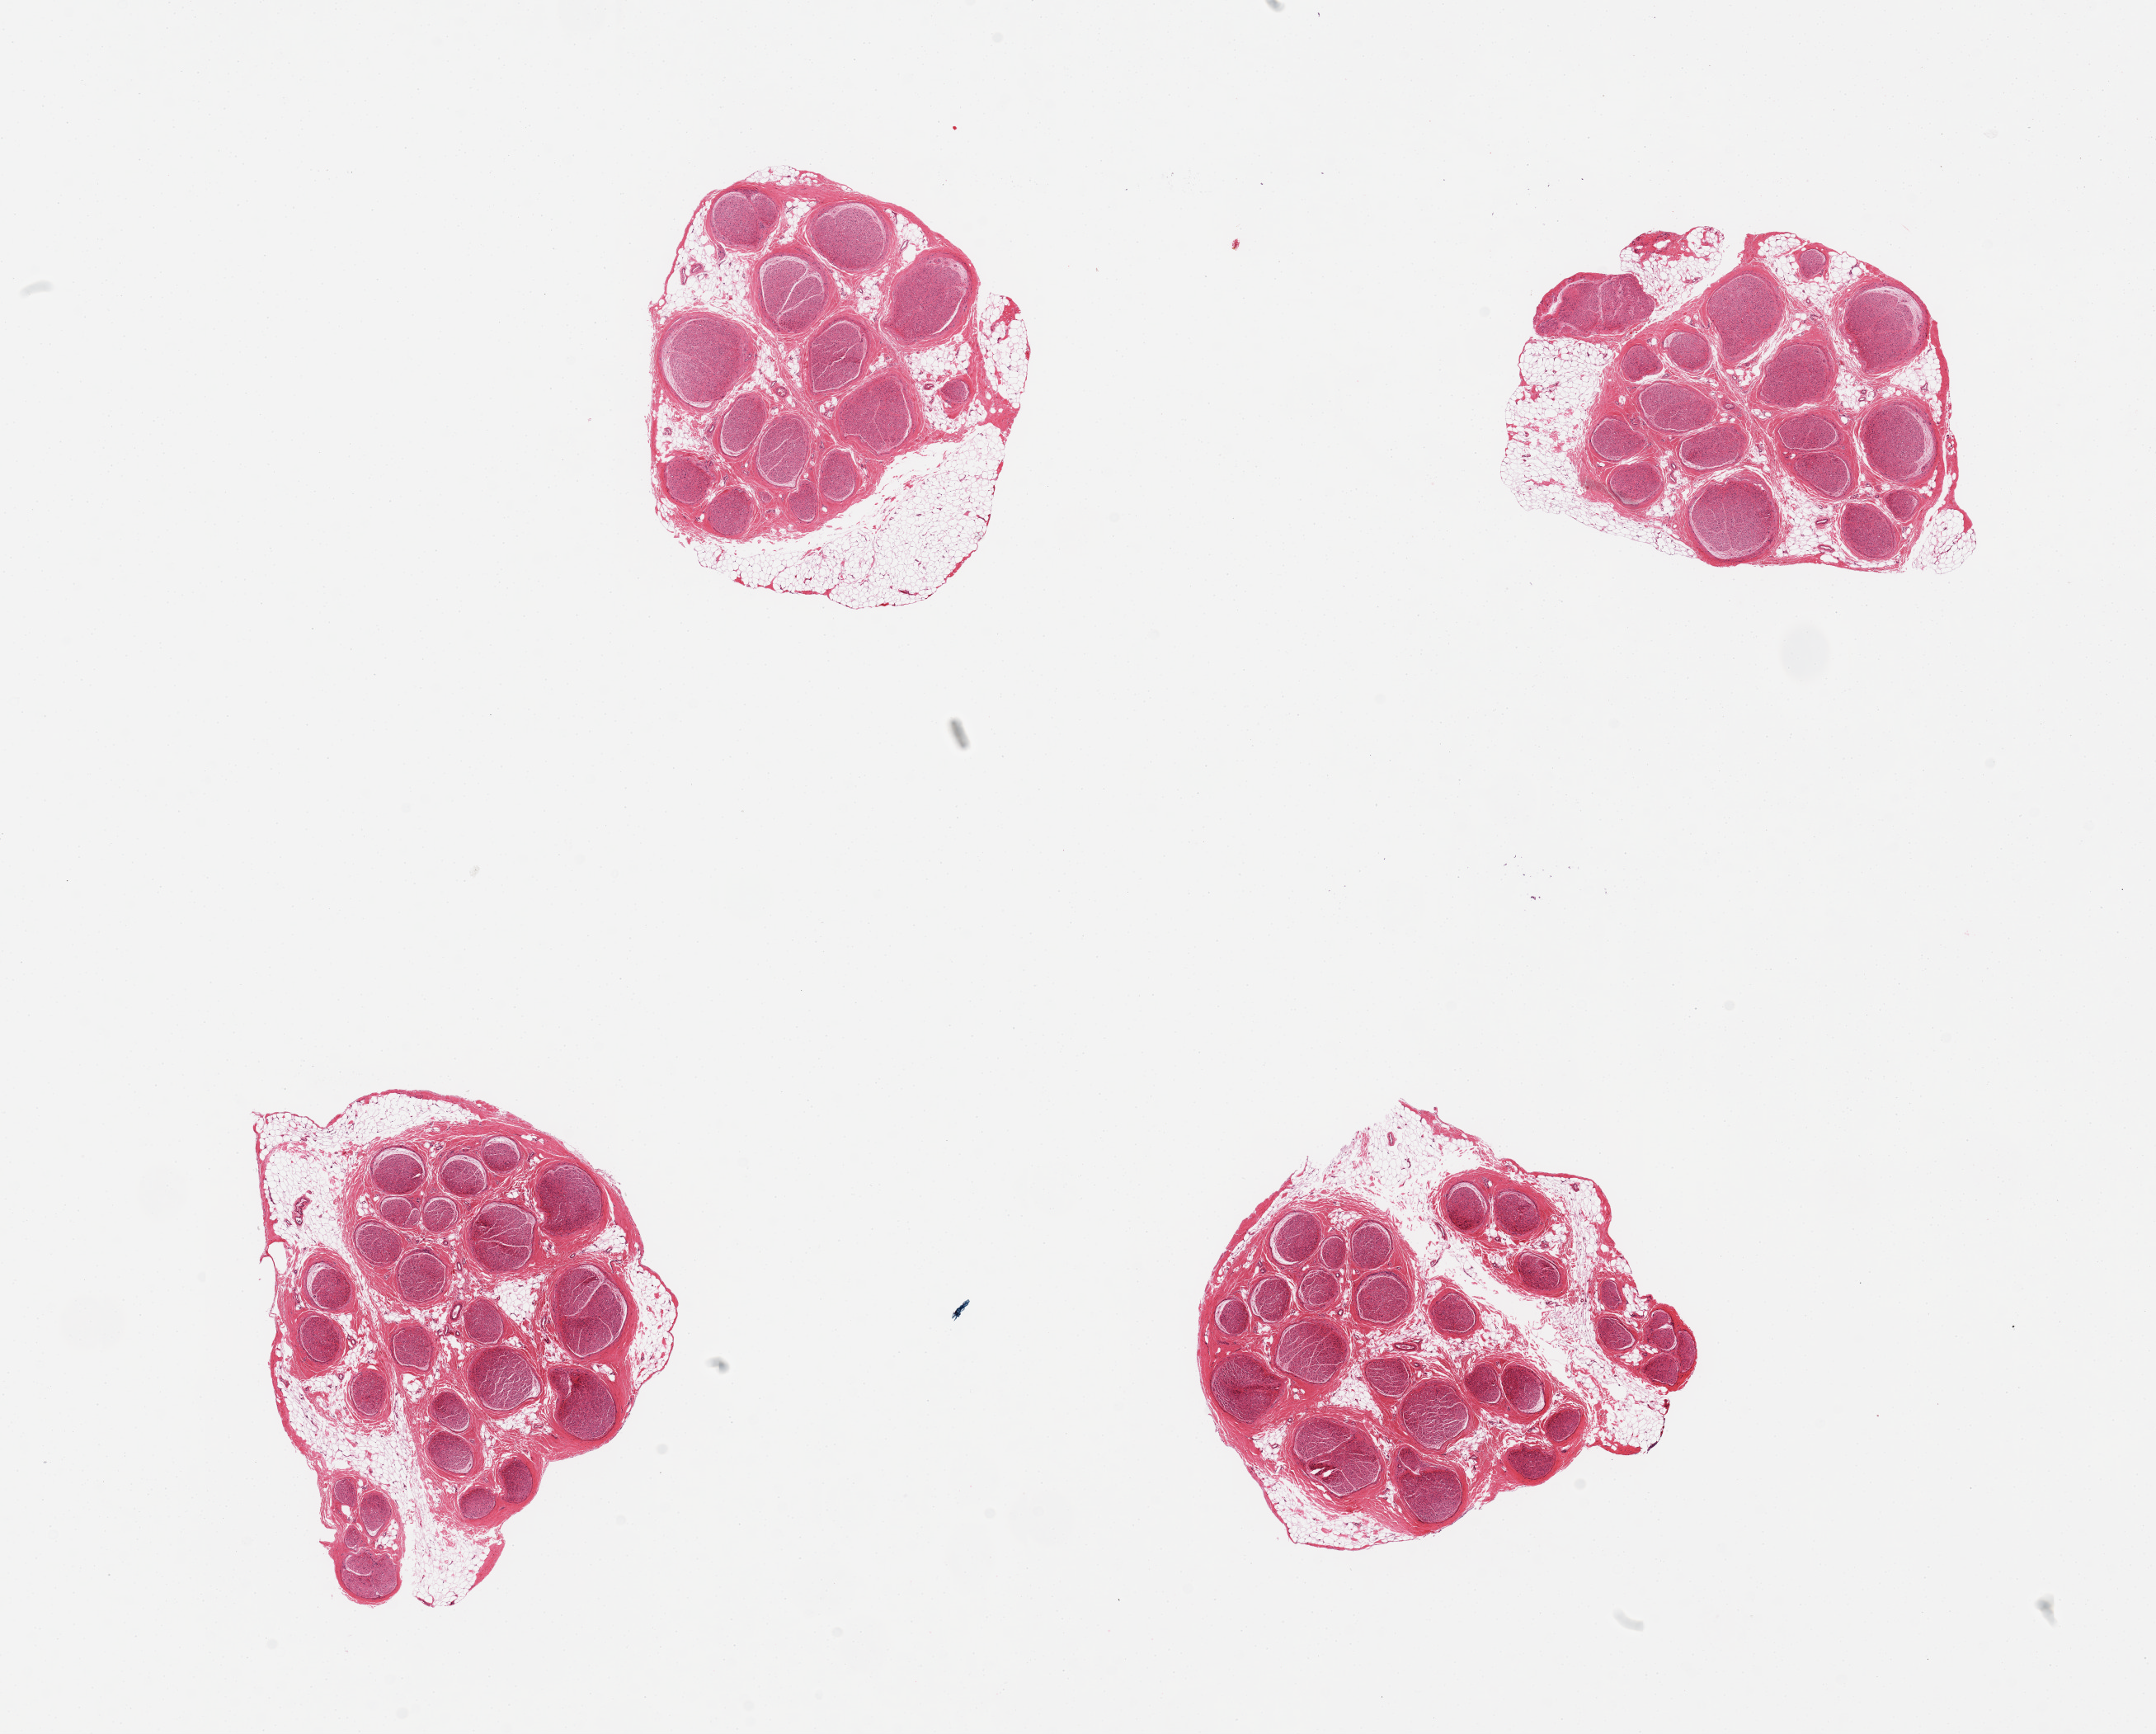
Whole-slide image, H&E stain, a low-resolution overview of the entire scanned area, about 20.7 x 16.6 mm (slide scanned at 20x). PAXgene-fixed, paraffin-embedded tissue. Target tissue: tibial nerve. Tissue donor sample. Donor sex: female.
Pathologist's review note for this sample: 4 pieces, each includes ~30% attached and internal fat.